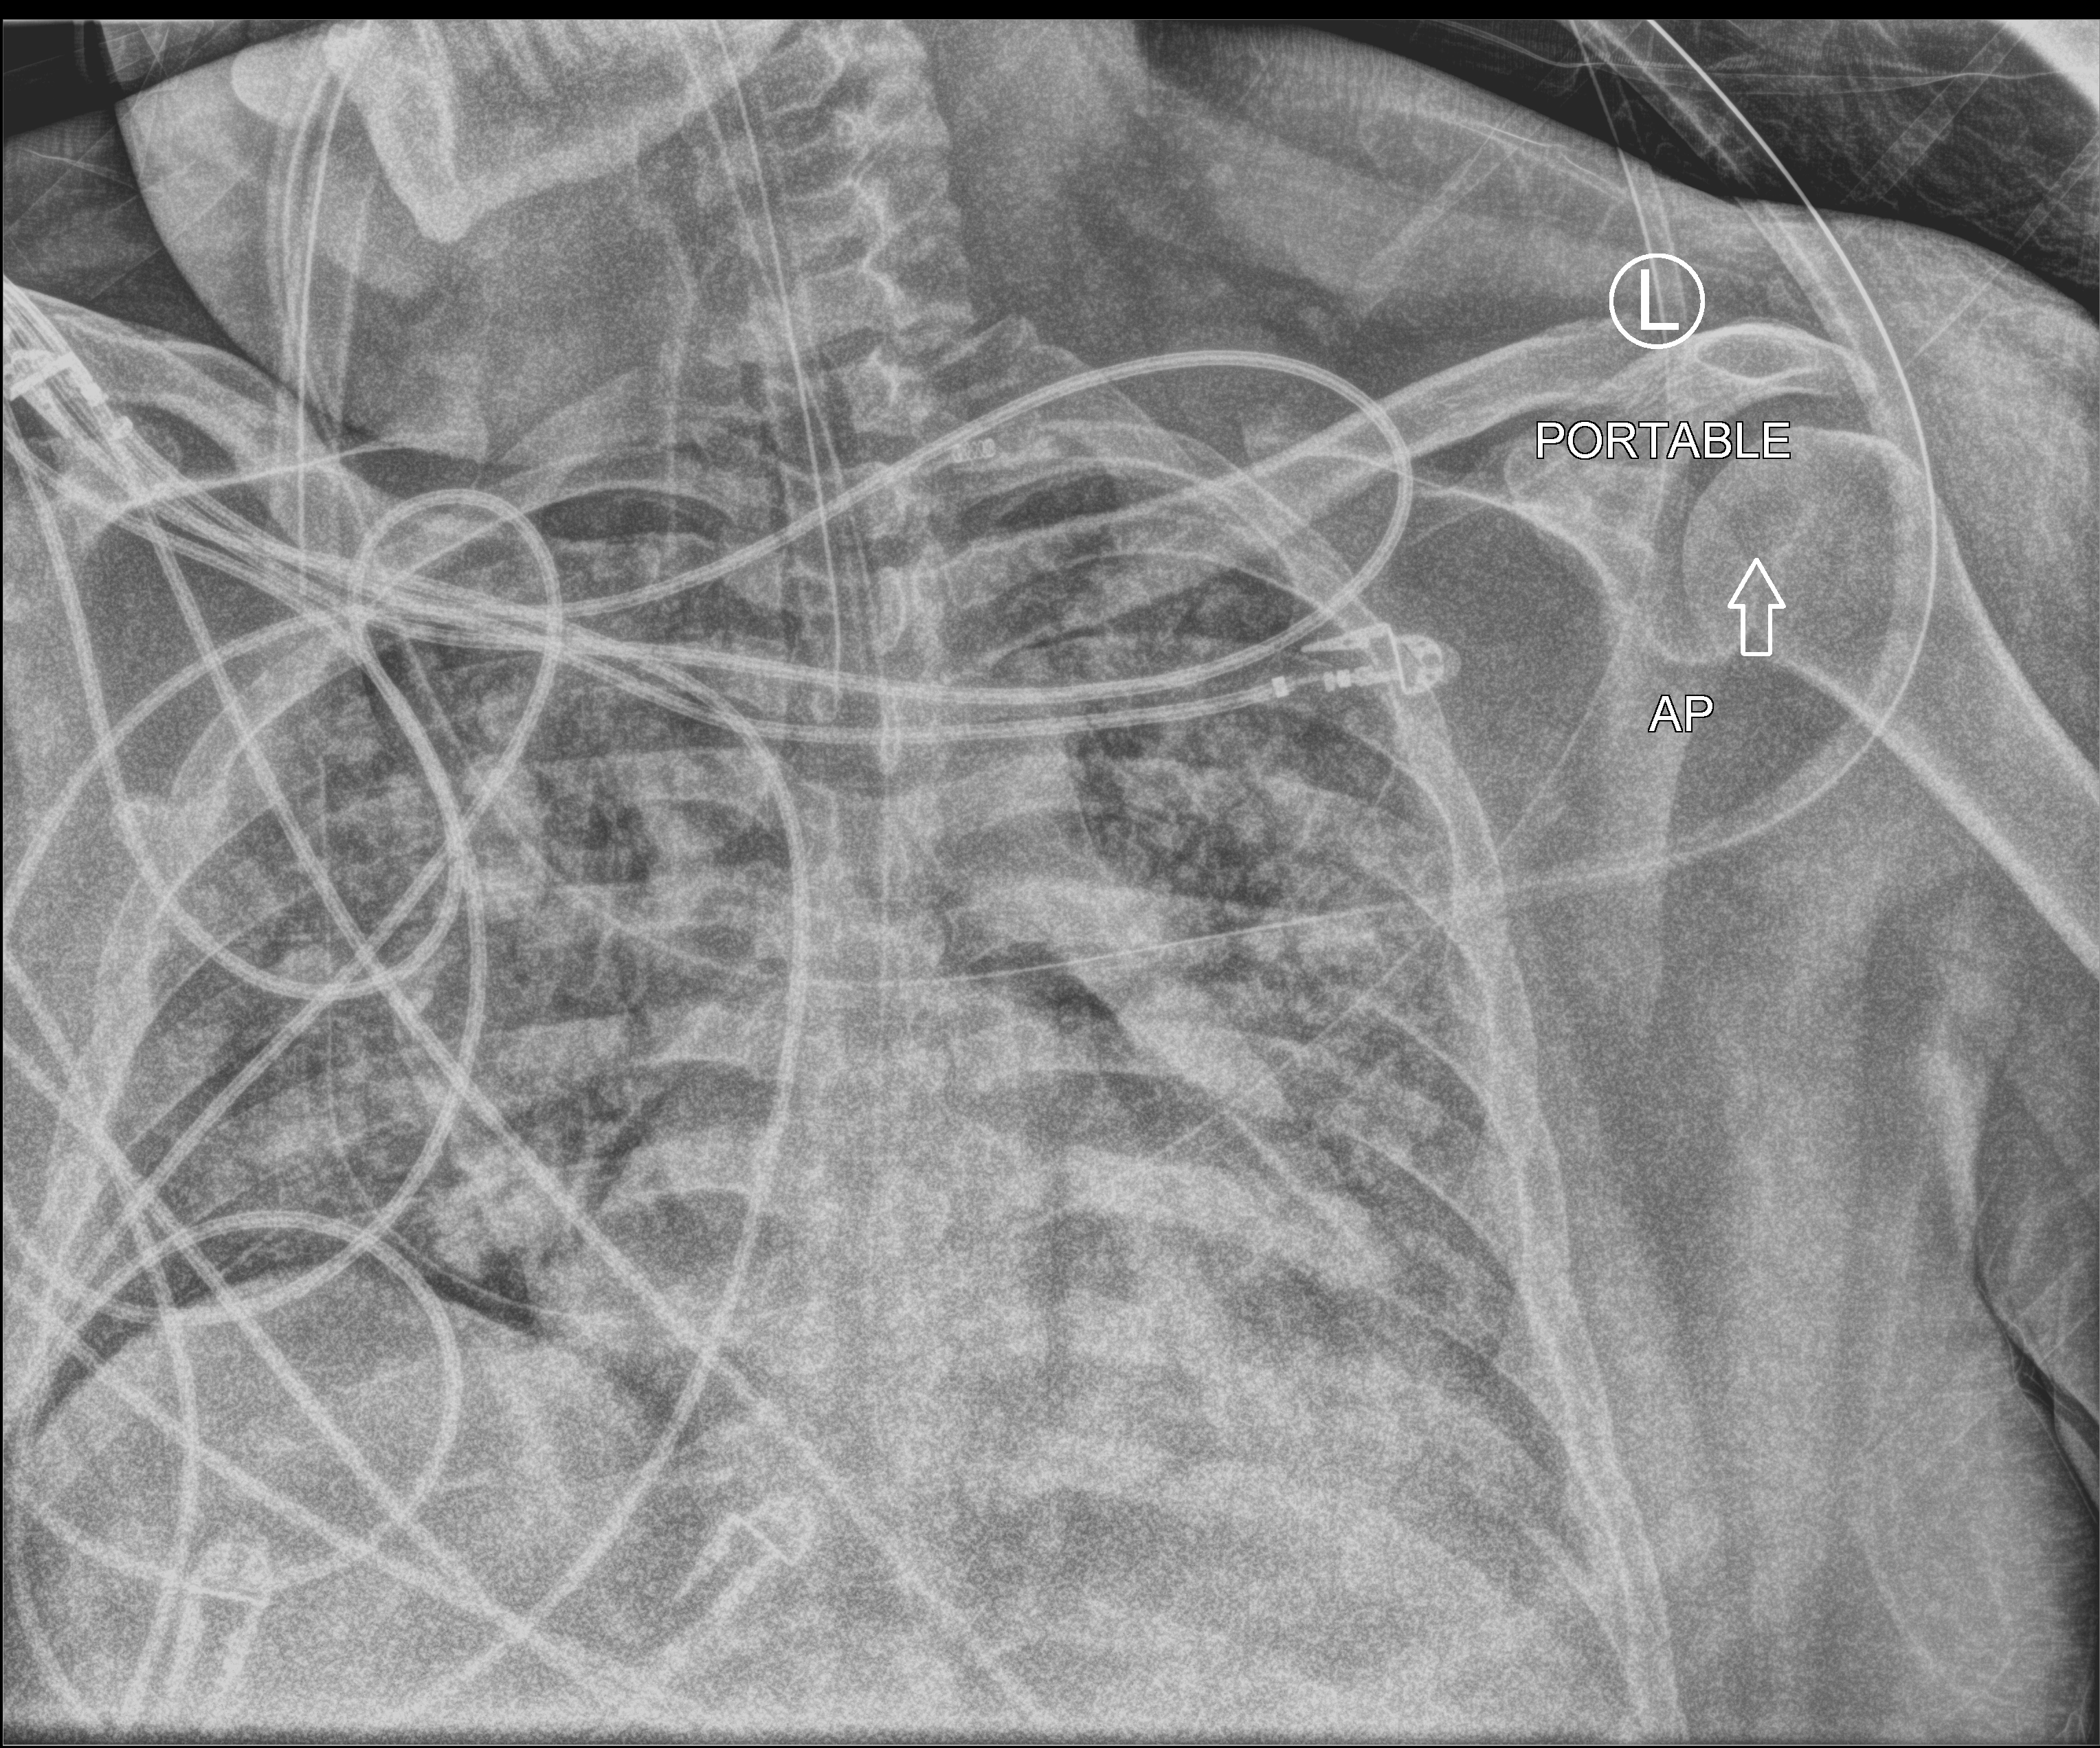
Portable chest radiograph, anteroposterior (AP) projection. Patient hospitalised with COVID-19, aged 18–59 years.
Admission-level facts for this patient (not findings on this image; timing relative to this image not recorded): mechanically ventilated during this hospital stay: yes; COPD (admission record): no.